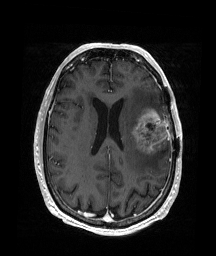
Brain MRI from a brain-tumour surgery series, one axial slice. Slice 75 of 176 in the series (ordered by position). T1-weighted post-contrast. 1 mm slice thickness. 216 × 256 image matrix. Case-level facts recorded for this patient, not image findings: histopathology: Glioblastoma; WHO grade: 4; IDH mutation: no.
Structures marked on this image (outlined manually by an expert reader):
- tumour: bounding box [x1, y1, x2, y2] px = [132, 109, 169, 155]